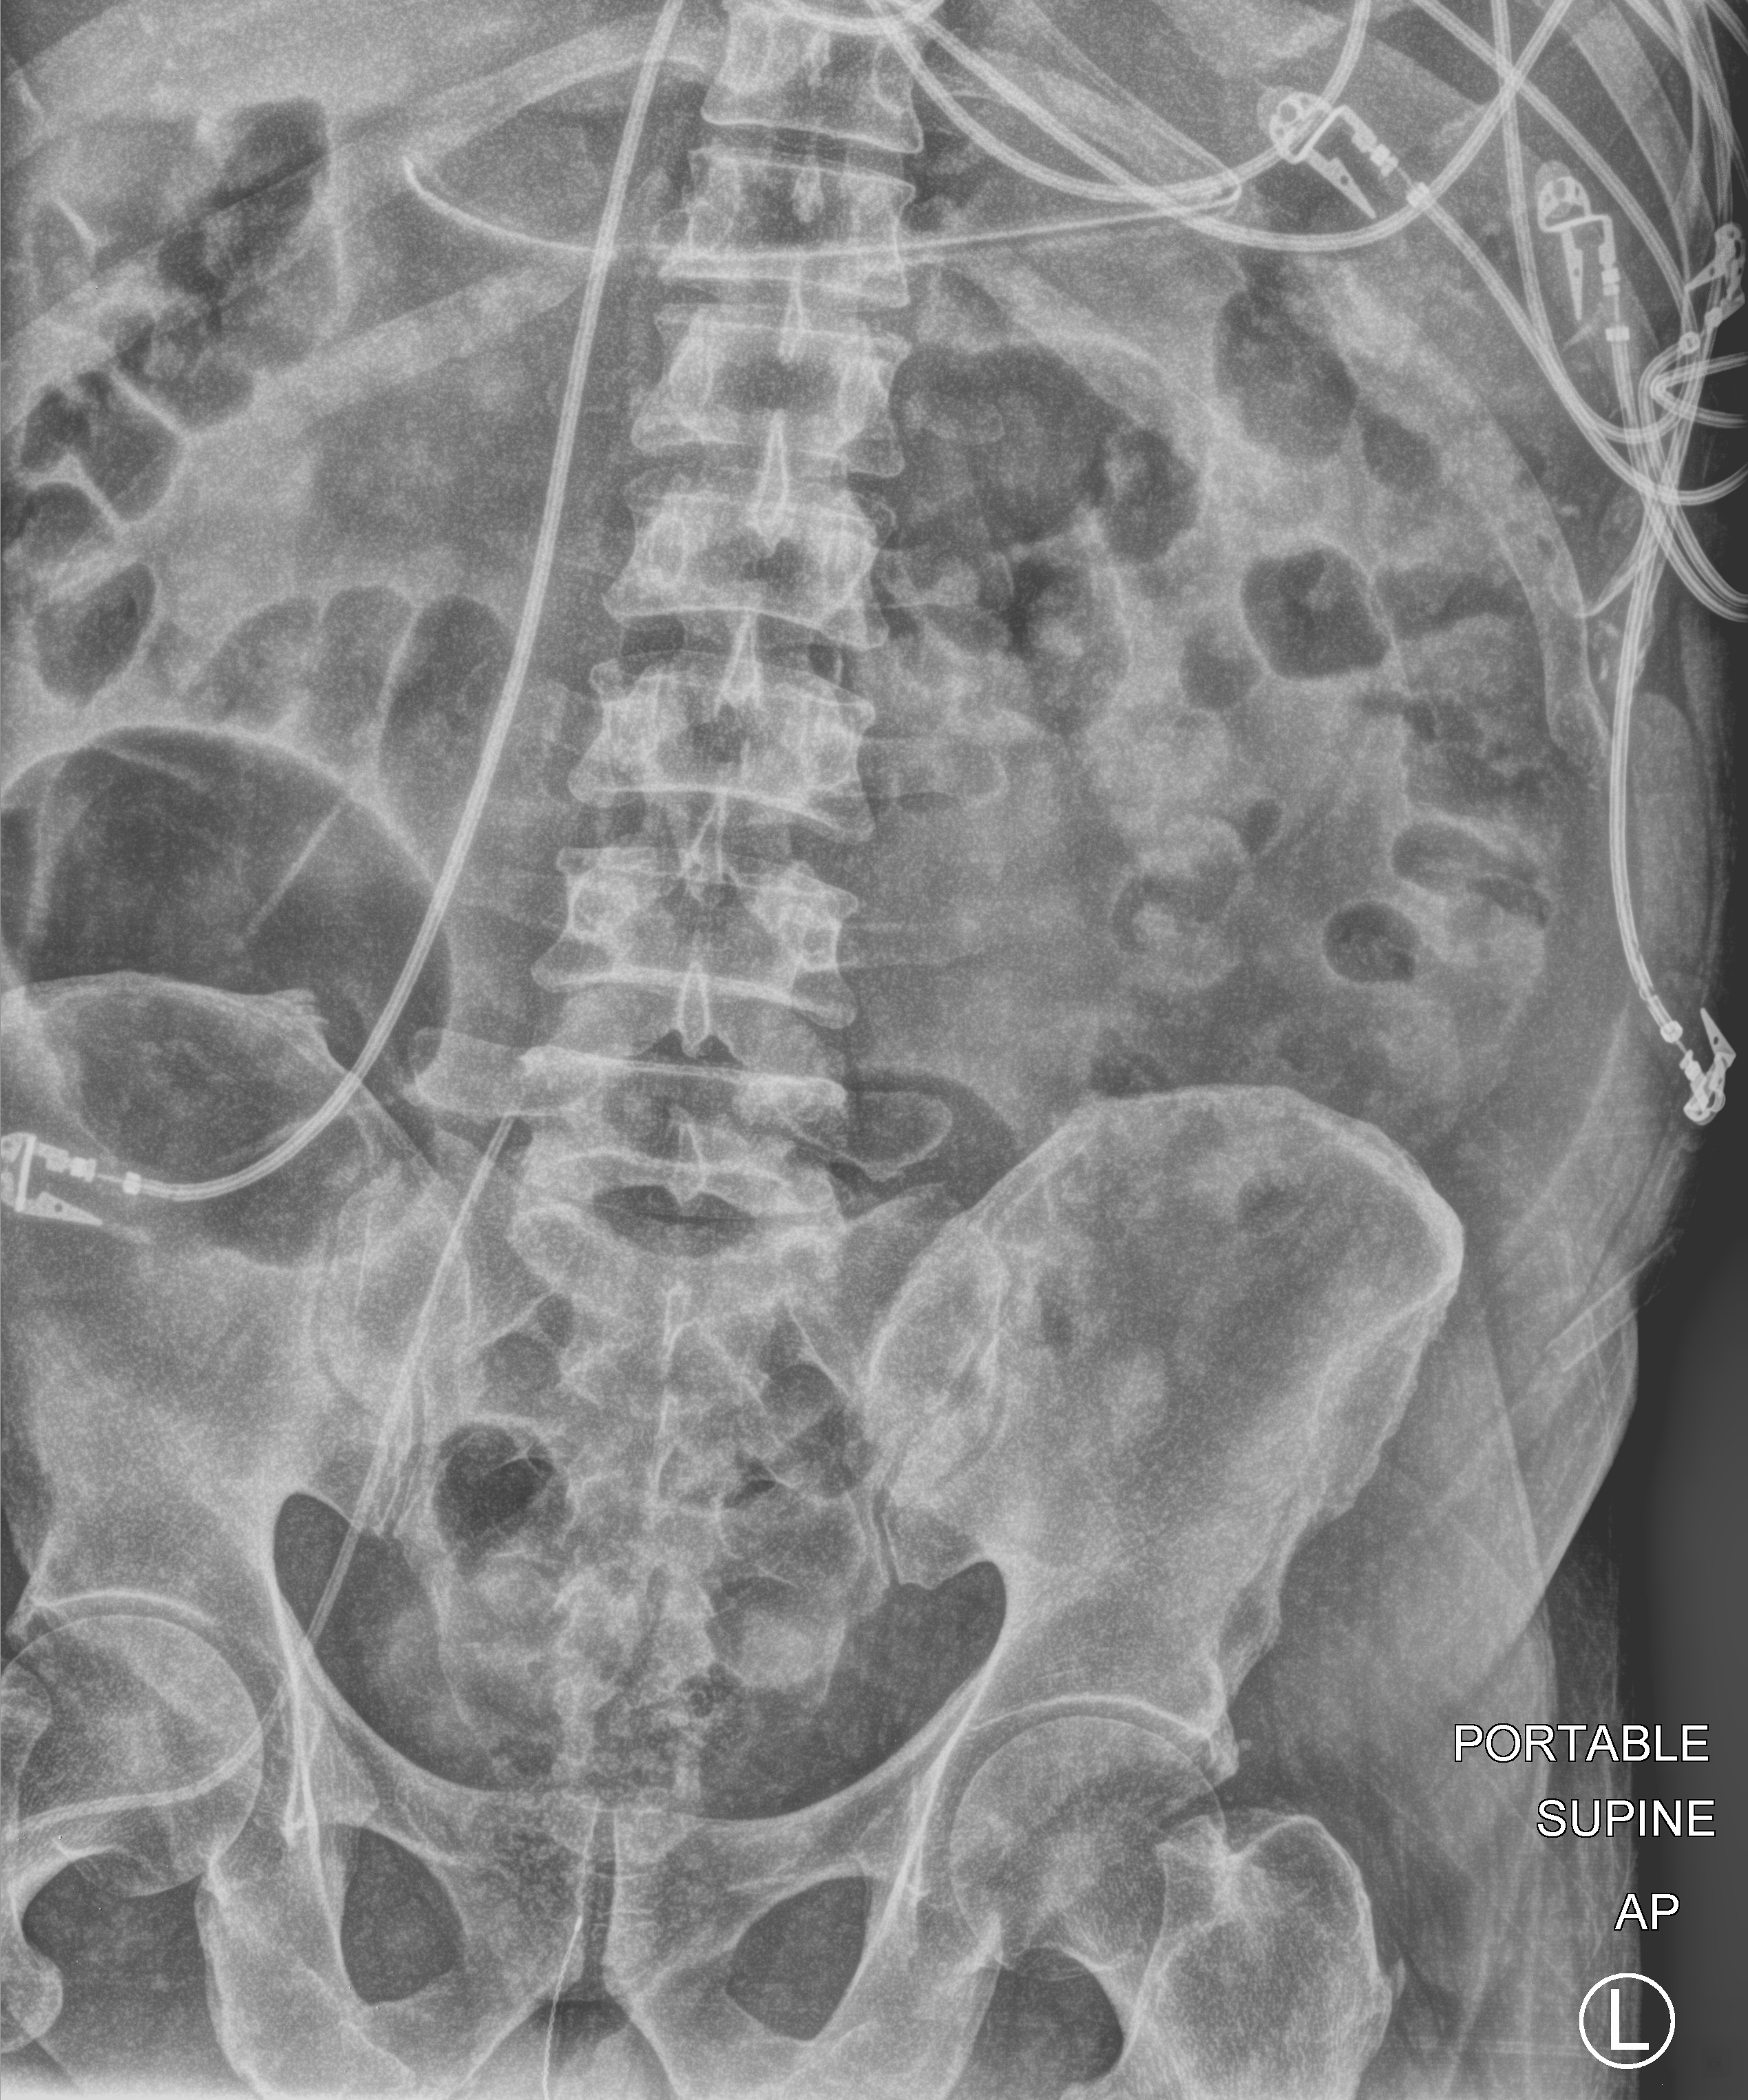
Bedside abdomen radiograph (computed radiography). Patient hospitalised with COVID-19; male, aged 18–59 years.
From the hospital-stay record, not from the radiograph (when in the stay this image was taken is not recorded):
- mechanically ventilated during this hospital stay: yes